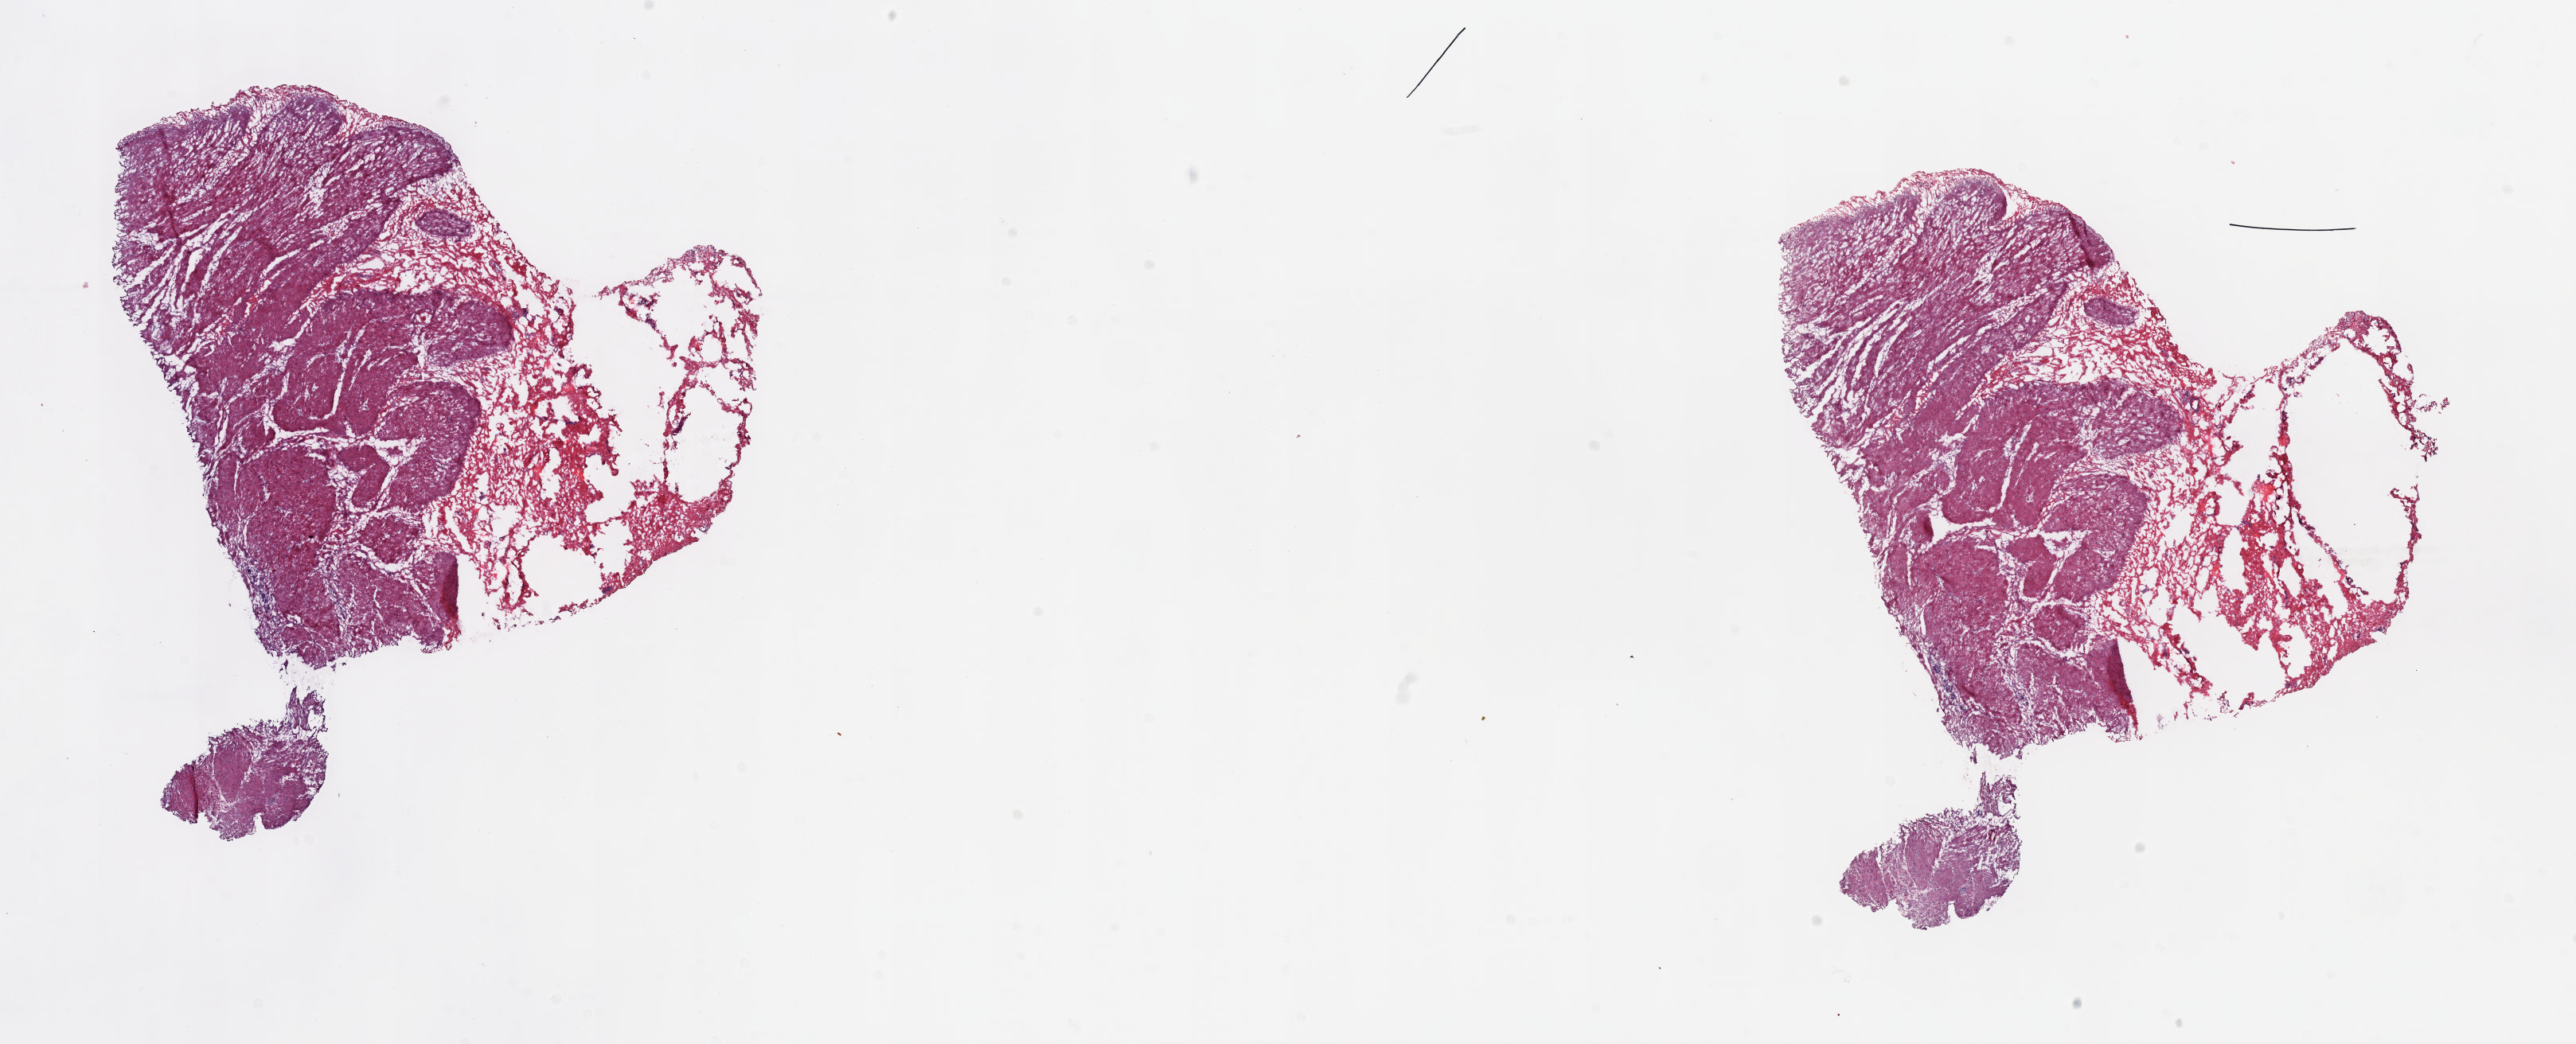
Digitized Hematoxylin and eosin (H&E) stained tissue section (whole slide) — a low-resolution overview of the entire scanned area, about 25.5 x 10.3 mm (acquisition: 20x scan), frozen section from the top of the tissue portion, stomach, solid tissue normal (non-tumour tissue) sample. Female patient; age at initial diagnosis 67 years. Pathologist review of this section (percent, as recorded): tumour cells 0%, tumour nuclei 0%, normal cells 100%, stromal cells 0%, necrosis 0%. Inflammatory infiltration, as recorded: lymphocyte infiltration 4%, monocyte infiltration 0%, neutrophil infiltration 0%.
This section: solid tissue normal sample (biorepository sample class). Patient diagnosis: Tubular adenocarcinoma (body of stomach).